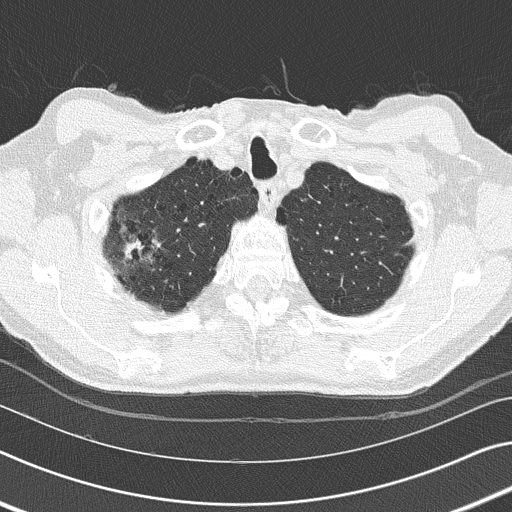
Low-dose screening chest CT, one axial slice; slice 140 of 155 in the series (ordered by position); 120 kVp; lung window (W 1500 / L -600 HU); 2 mm slice thickness; 512 × 512 image matrix.
Outlined on this slice (manually delineated by an expert):
- lesion 1 (tumor, middle lobe of right lung): box from (x=122, y=235) to (x=161, y=266) px